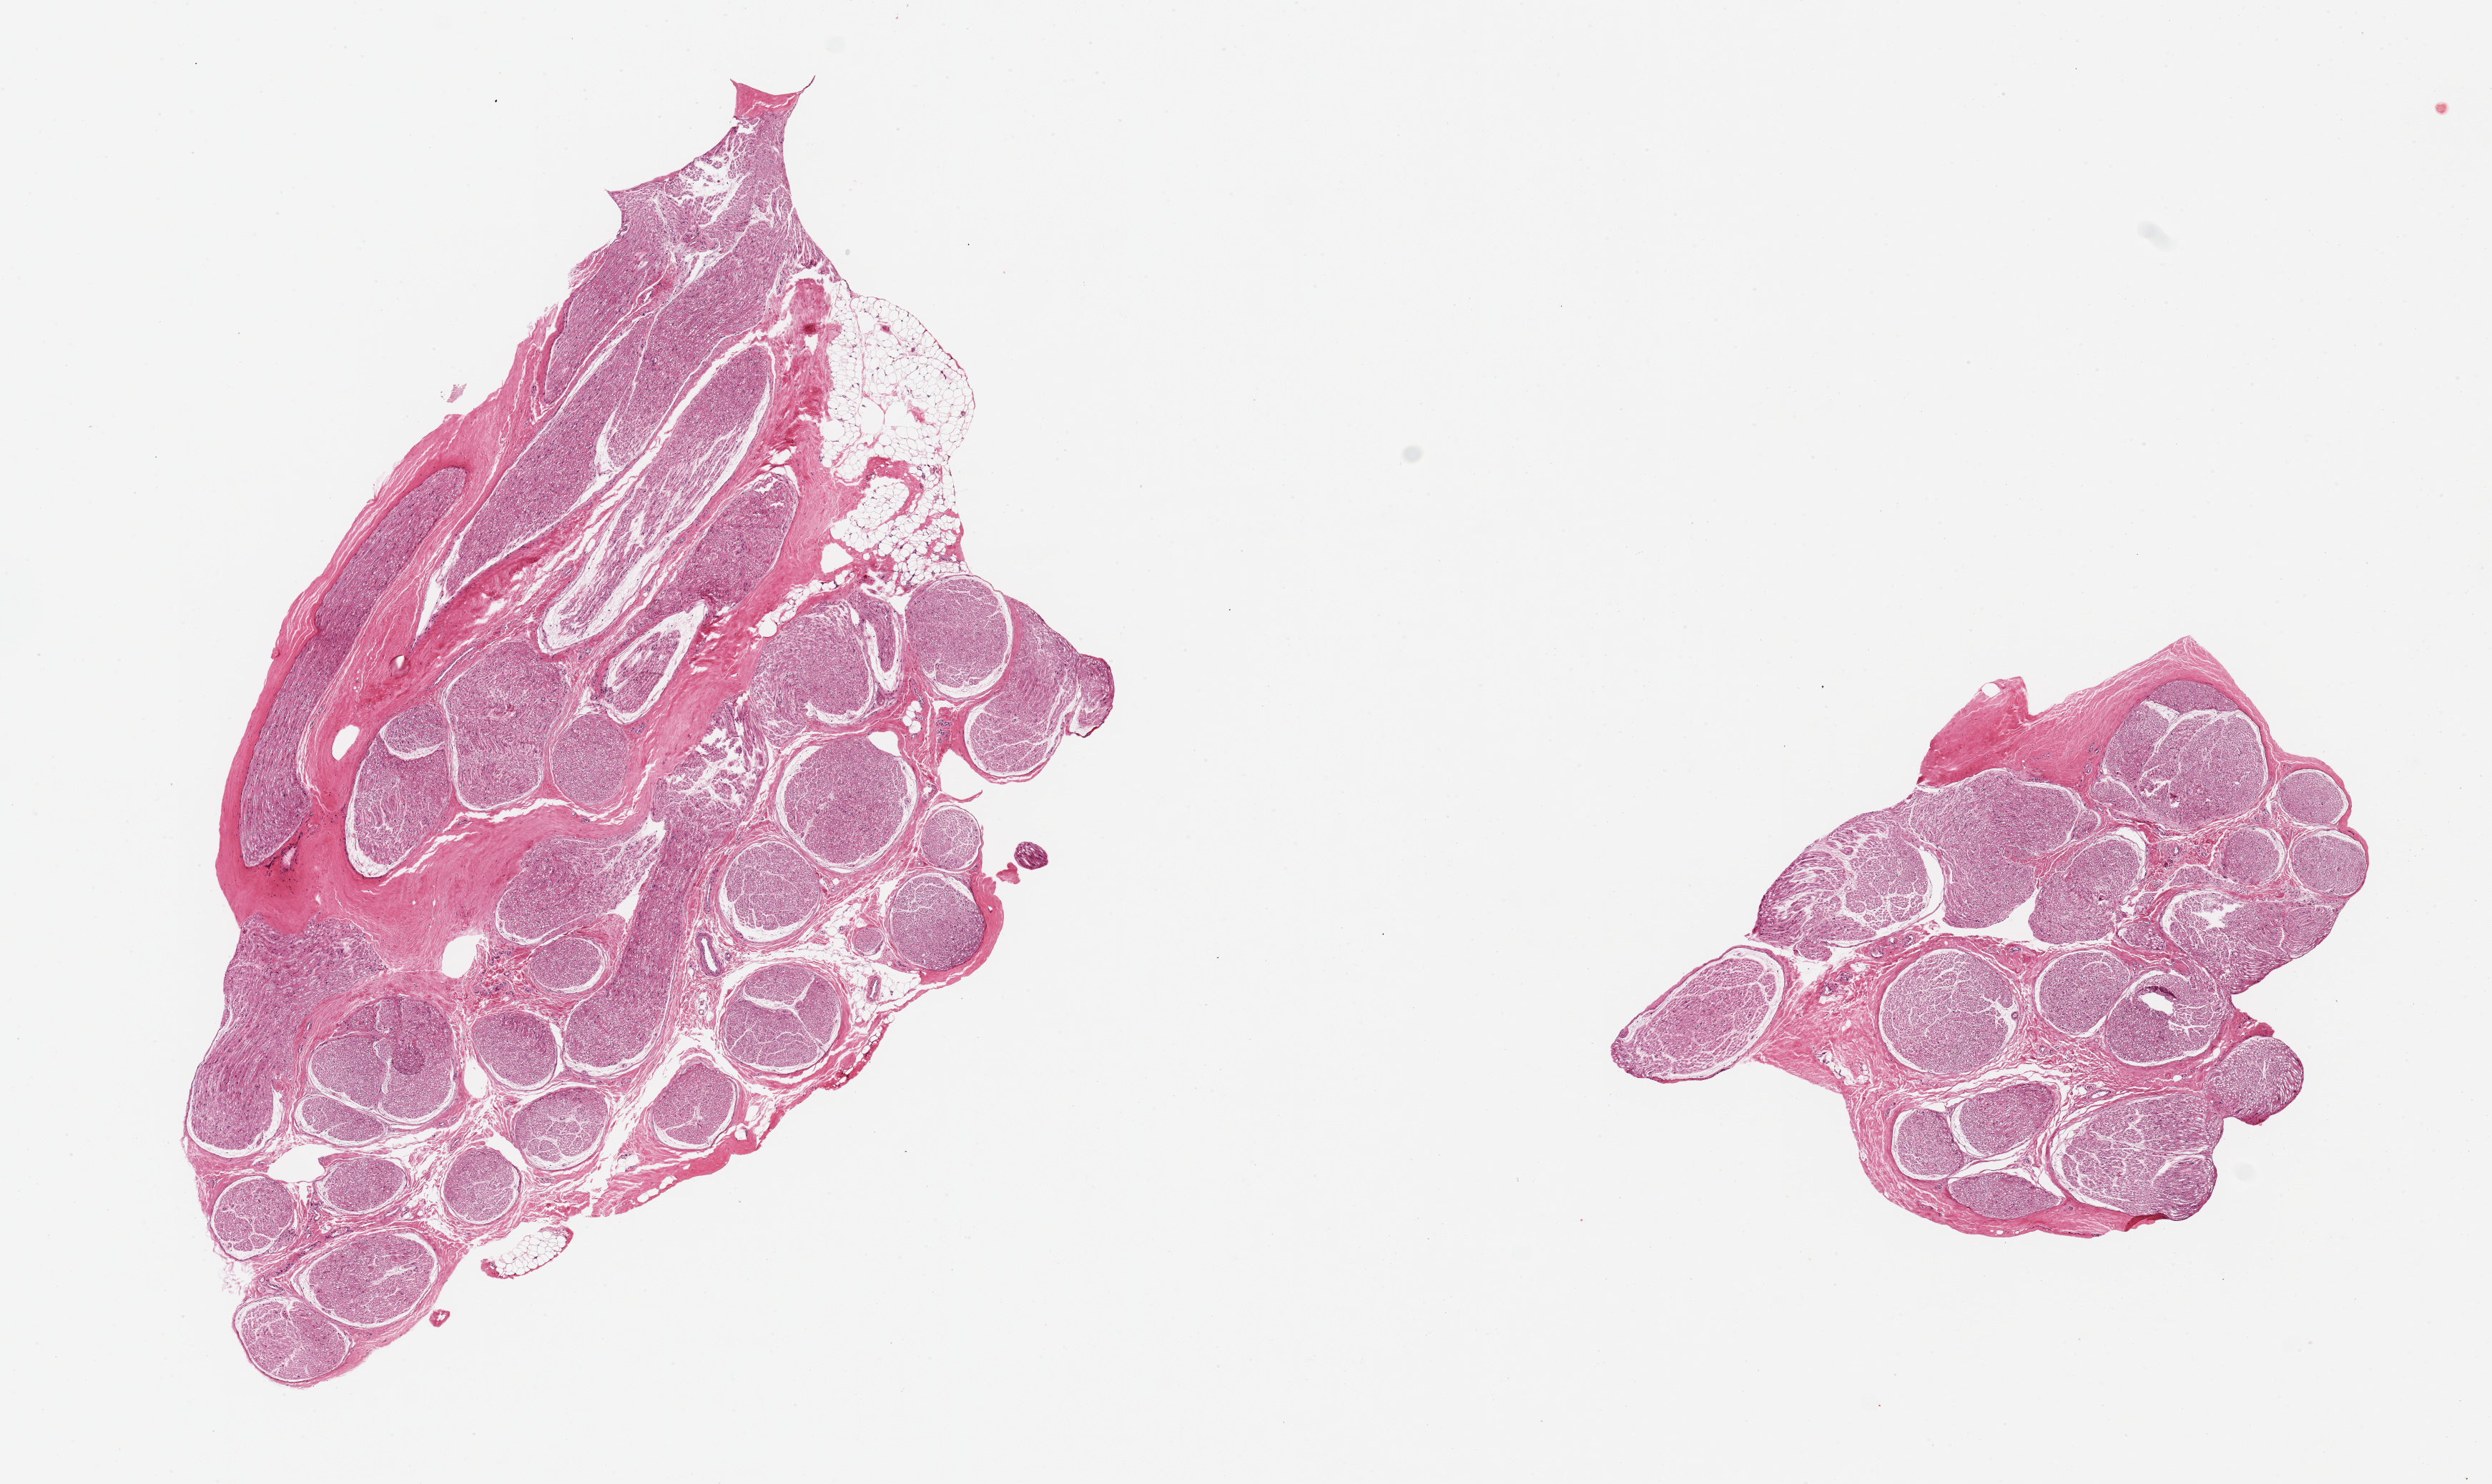
Whole-slide image, H&E stain, whole scanned area (about 13.8 x 8.2 mm, from a 20x scan) shown as a low-resolution overview, PAXgene-fixed paraffin-embedded (PFPE) section, sampled site (target tissue): tibial nerve, tissue donor sample. Donor sex: female.
Review note (as recorded): 2 pieces 6x4 & 3x3 mm; <10% adipose in larger.